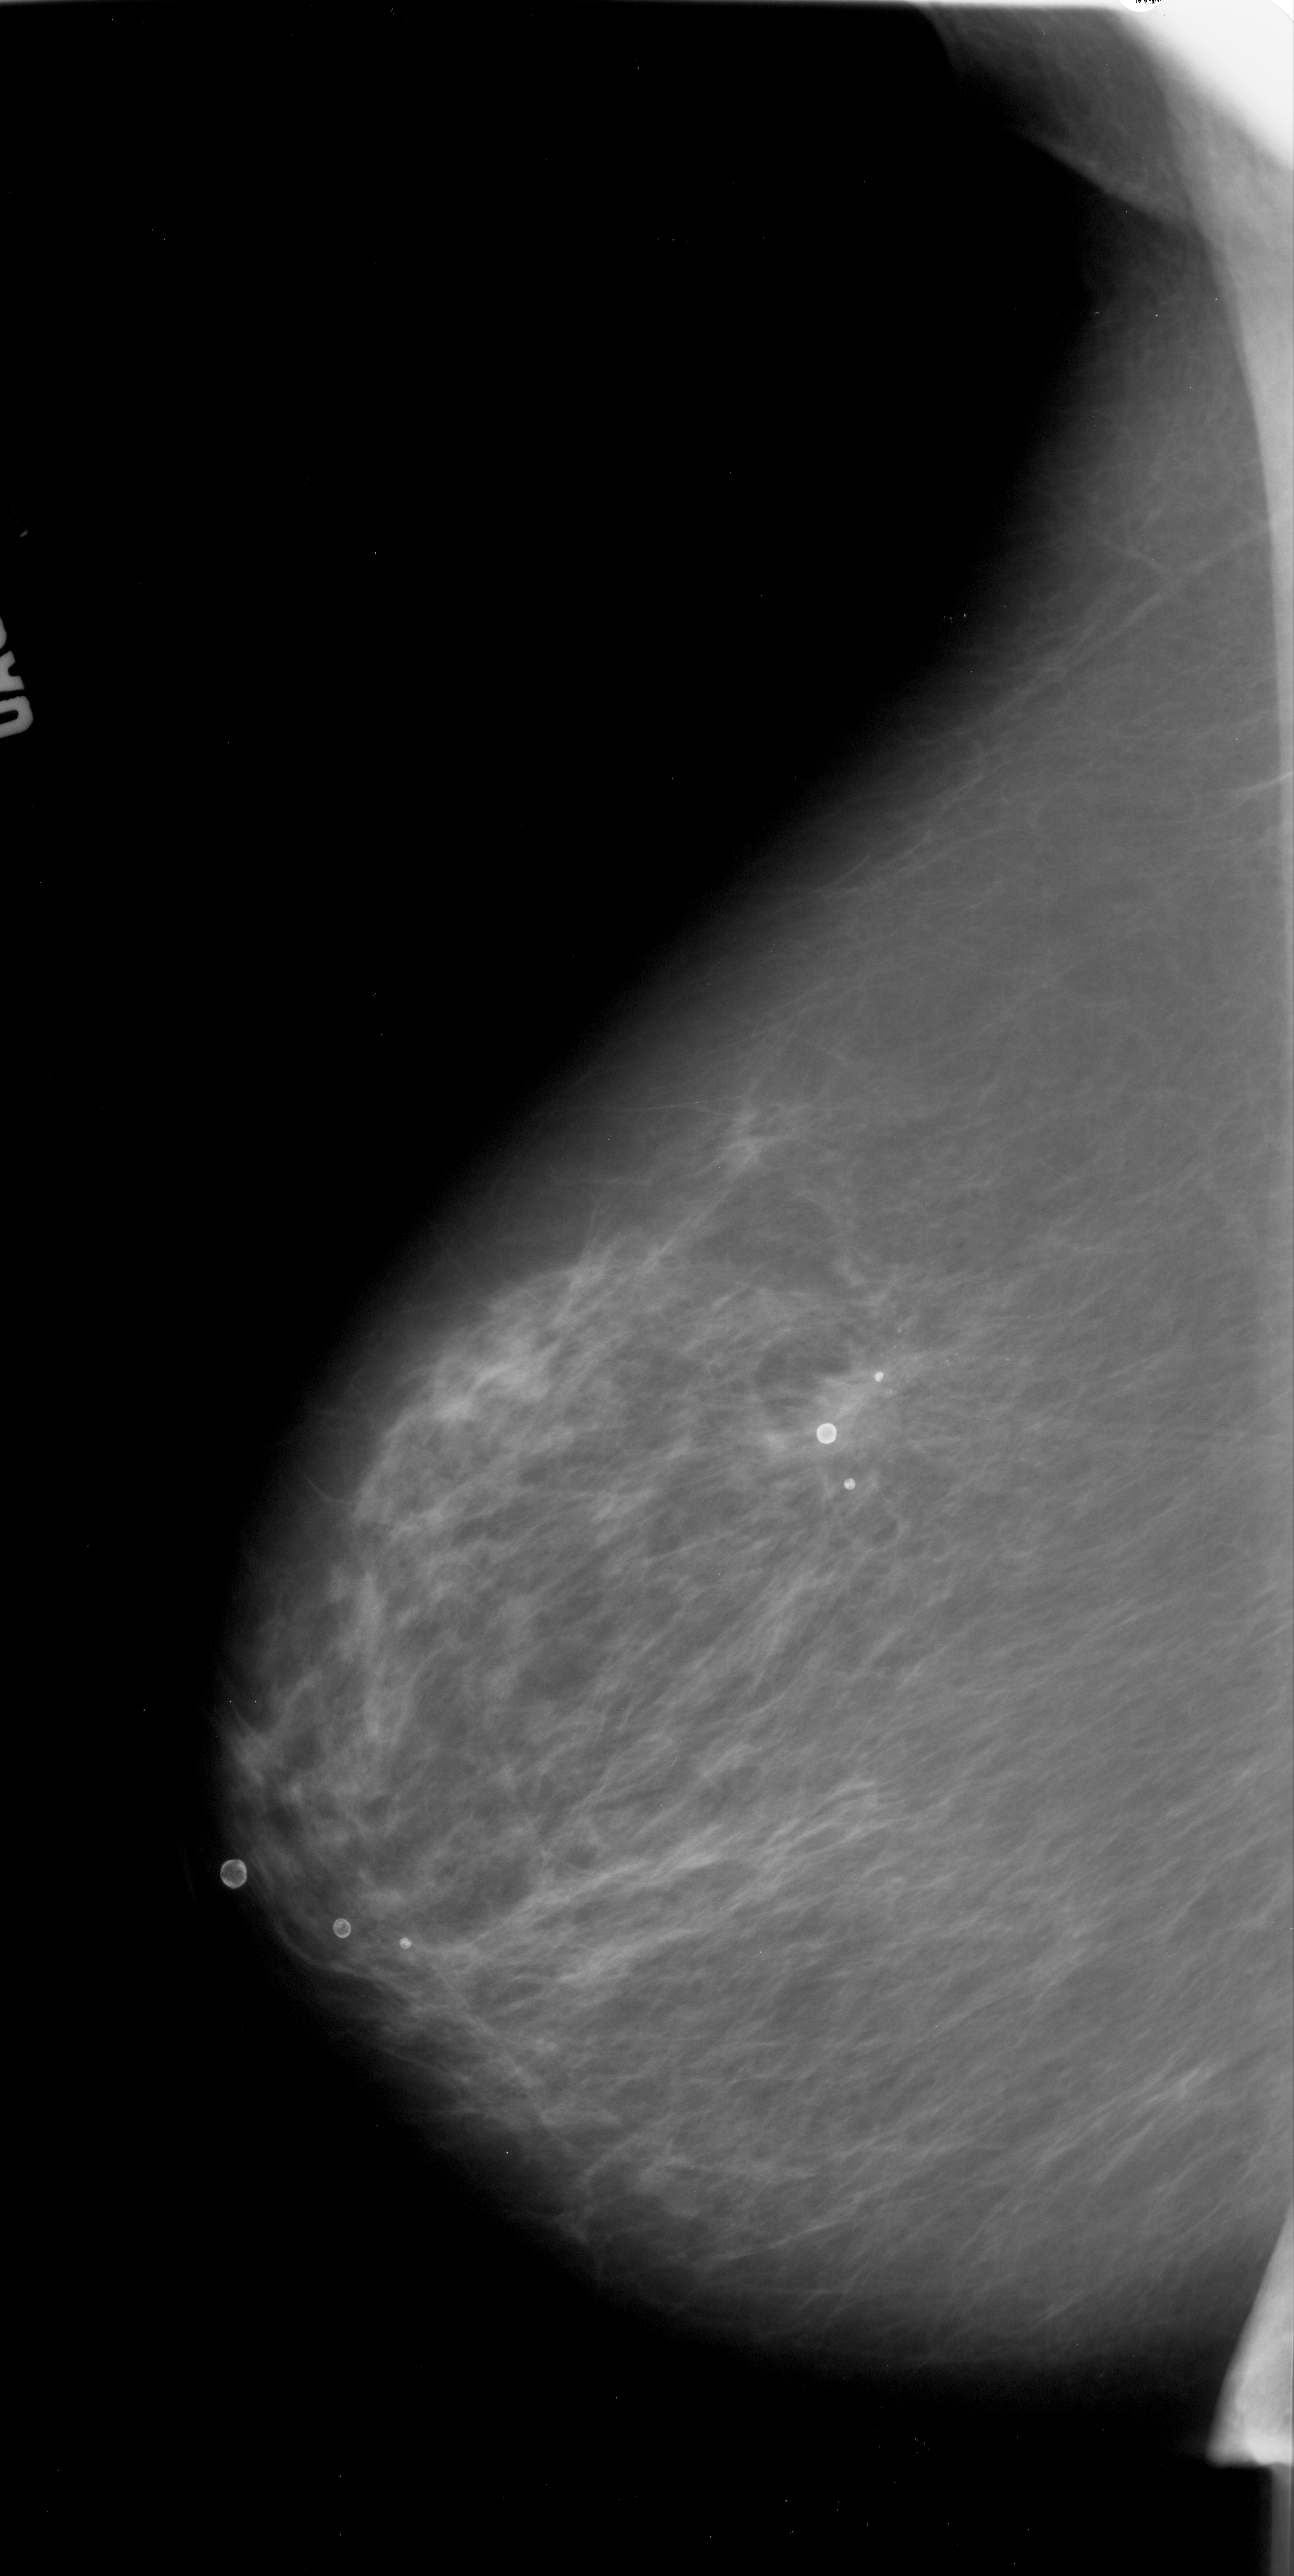
Digitized screen-film mammogram; left breast; mediolateral oblique (MLO) view; BI-RADS breast density category 2 (scale 1–4); 1294 × 2576 image matrix.
Expert-marked regions of interest on this film, with their recorded descriptors:
- calcifications, morphology pleomorphic, distribution linear; BI-RADS assessment category 4; pathology (as recorded): malignant: bounding box [x1, y1, x2, y2] px = [828, 1304, 1046, 1456]